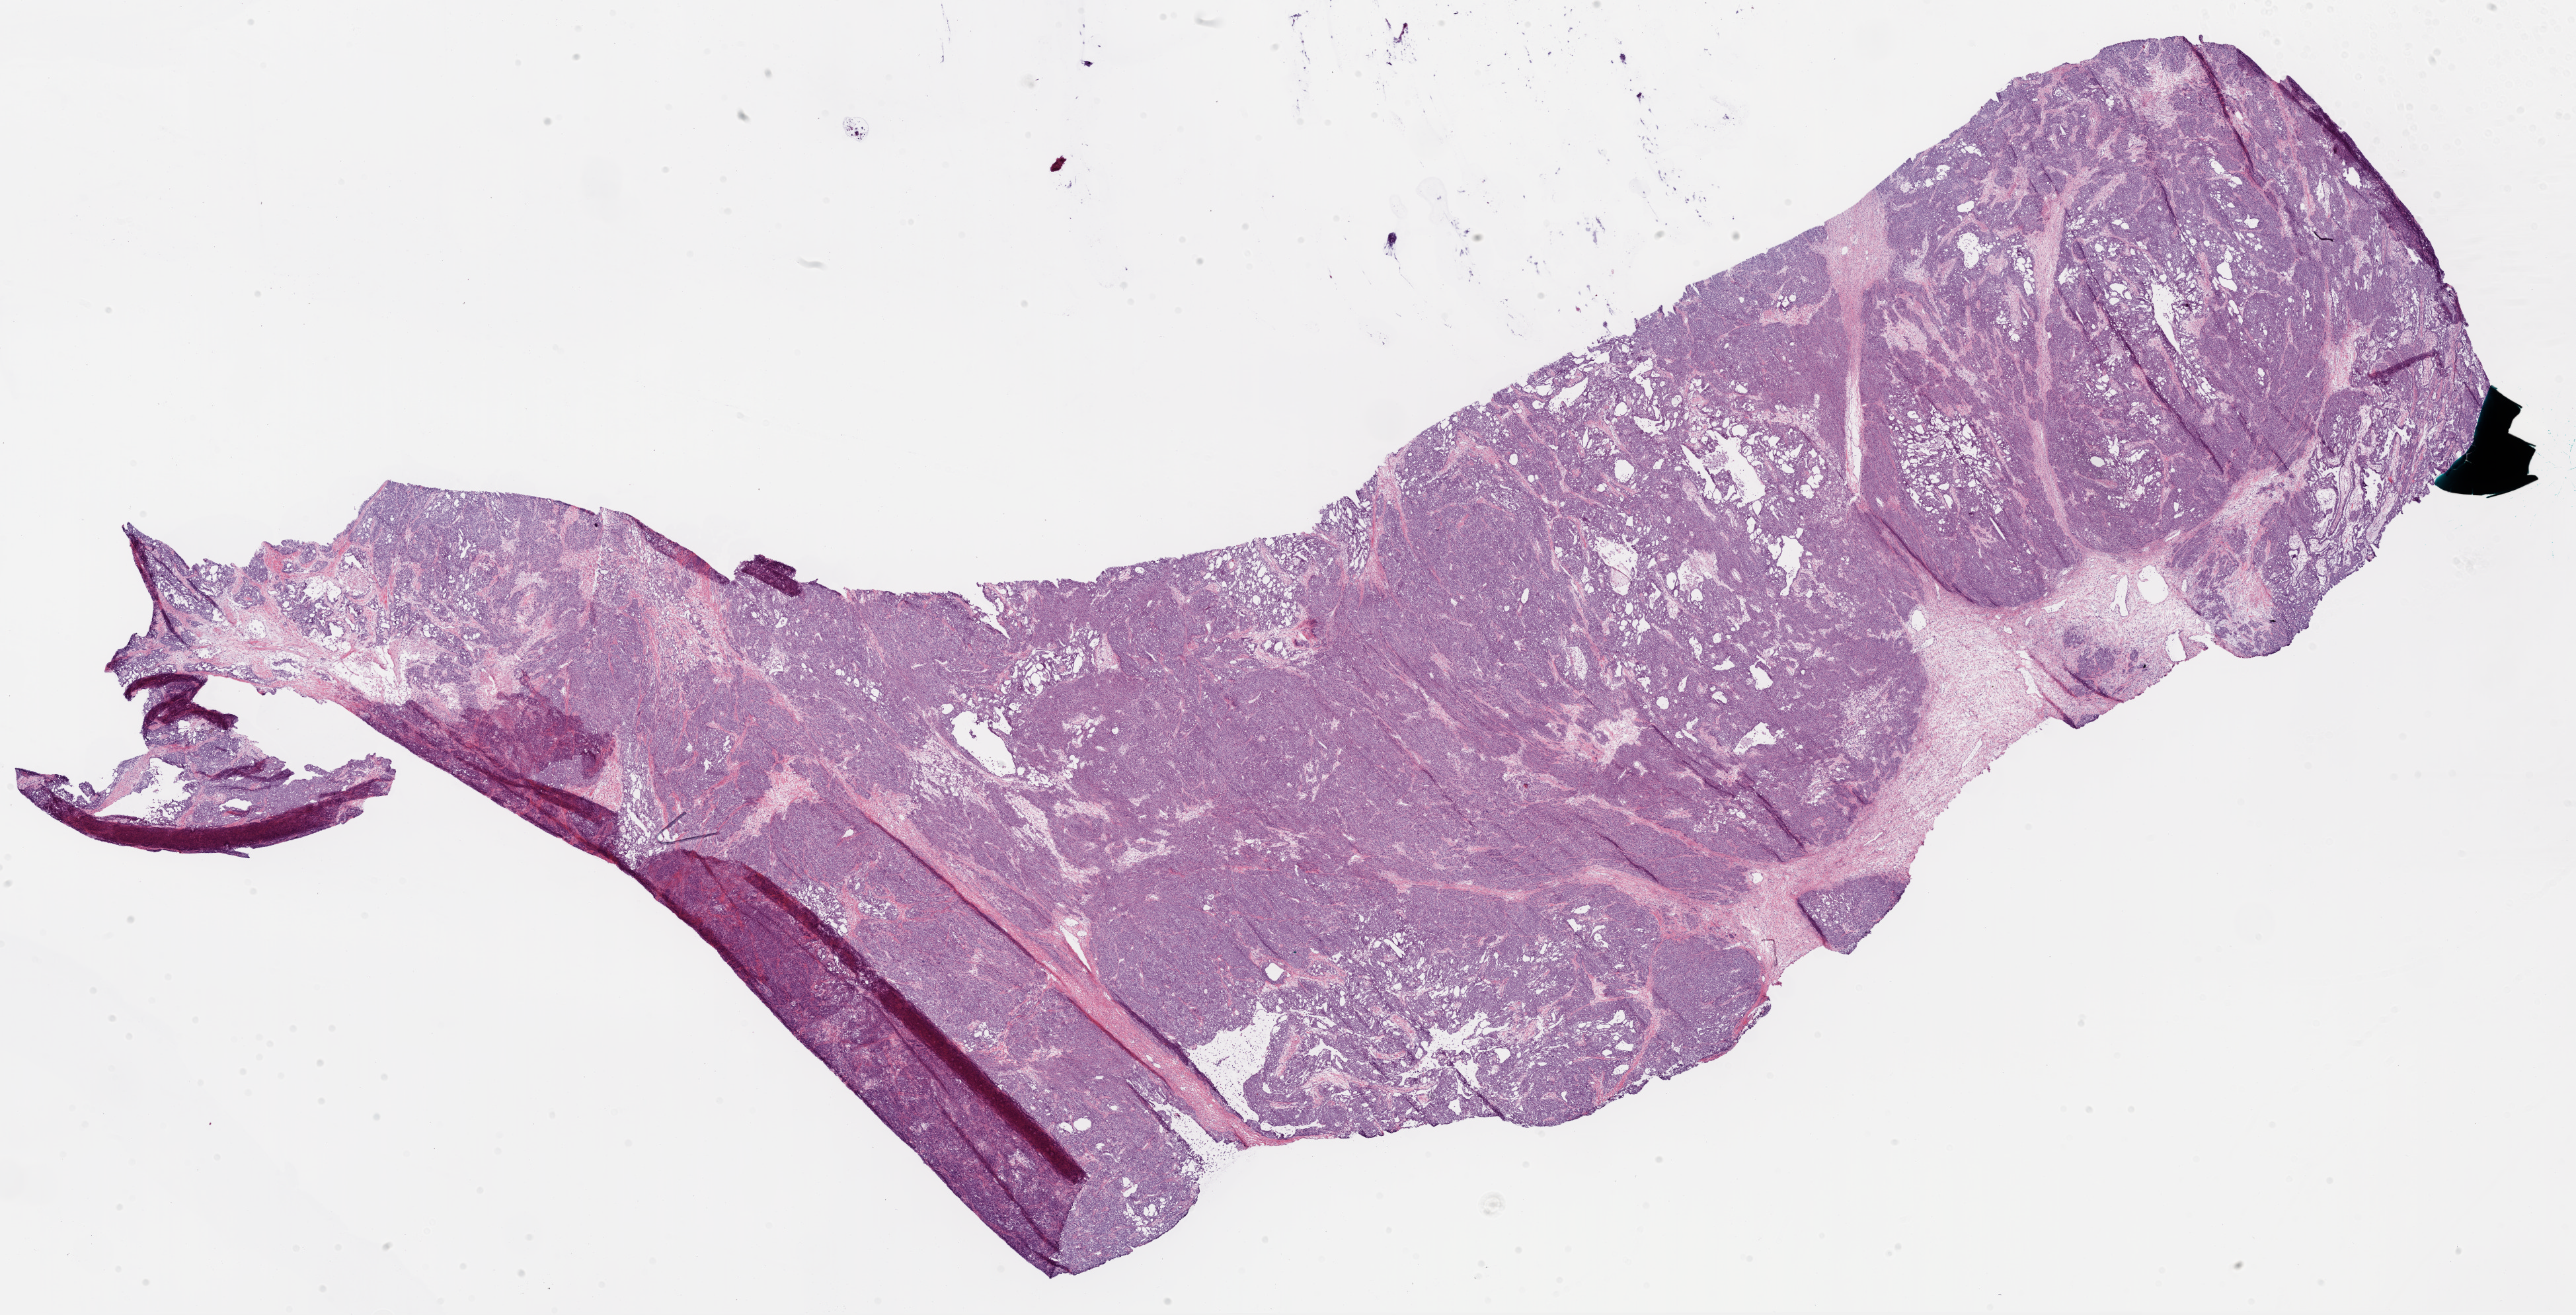
Whole-slide histology image, H&E — whole scanned area (about 31.4 x 16.0 mm, from a 20x scan) shown as a low-resolution overview, frozen section, sample: primary tumour, ovary. Patient: female, age at initial diagnosis 69 years.
Pathologic diagnosis: Serous cystadenocarcinoma, NOS.